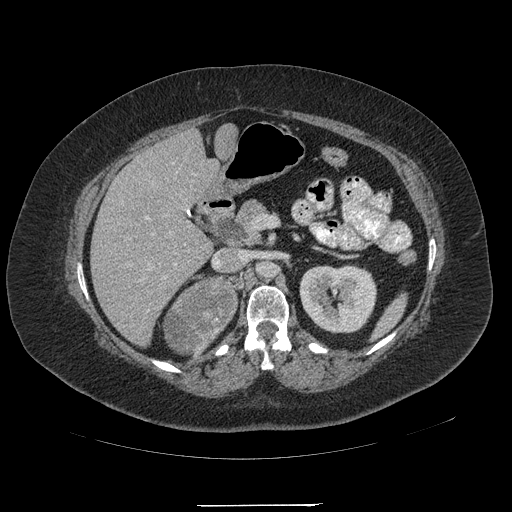
Contrast-enhanced abdominal CT, one axial slice; slice 118 of 217 in the series (ordered by position); reconstruction kernel STANDARD; intravenous contrast given; soft-tissue window (W 400 / L 40 HU); 1.25 mm slice thickness; 512 × 512 image matrix, field of view 453 × 453 mm. Female patient, age 55 years. From the clinical record (not read from this slice): diagnosis: adrenocortical carcinoma; tumour side: right adrenal; tumour size at pathology: 11 cm; Ki-67 index: 20 %; stage (as recorded): 2.
Structures marked on this image (semi-automatic segmentation, software-assisted and operator-edited):
- mass: bounding box [x1, y1, x2, y2] px = [165, 279, 237, 353]